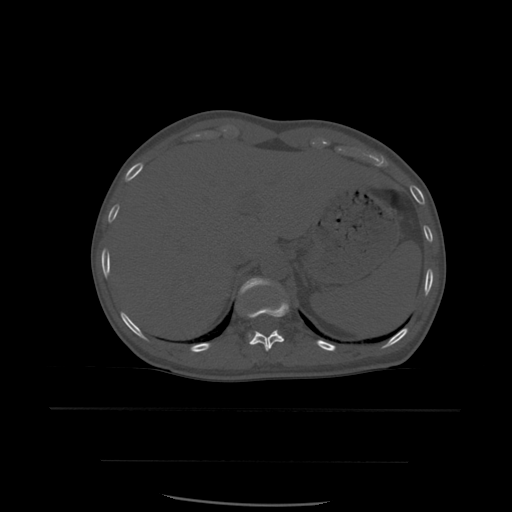
CT including the spine, one axial slice. Position 290 of 574 along the scan axis. Bone window (W 1800 / L 400 HU). 512 × 512 image matrix. Patient age 48 years. From the clinical record (not read from this slice): primary cancer: lung.
Outlined on this slice (semi-automatic segmentation, software-assisted and operator-edited):
- T11 vertebra: box from (x=244, y=299) to (x=289, y=352) px
- T12 vertebra: (x=240, y=278)–(x=272, y=337)